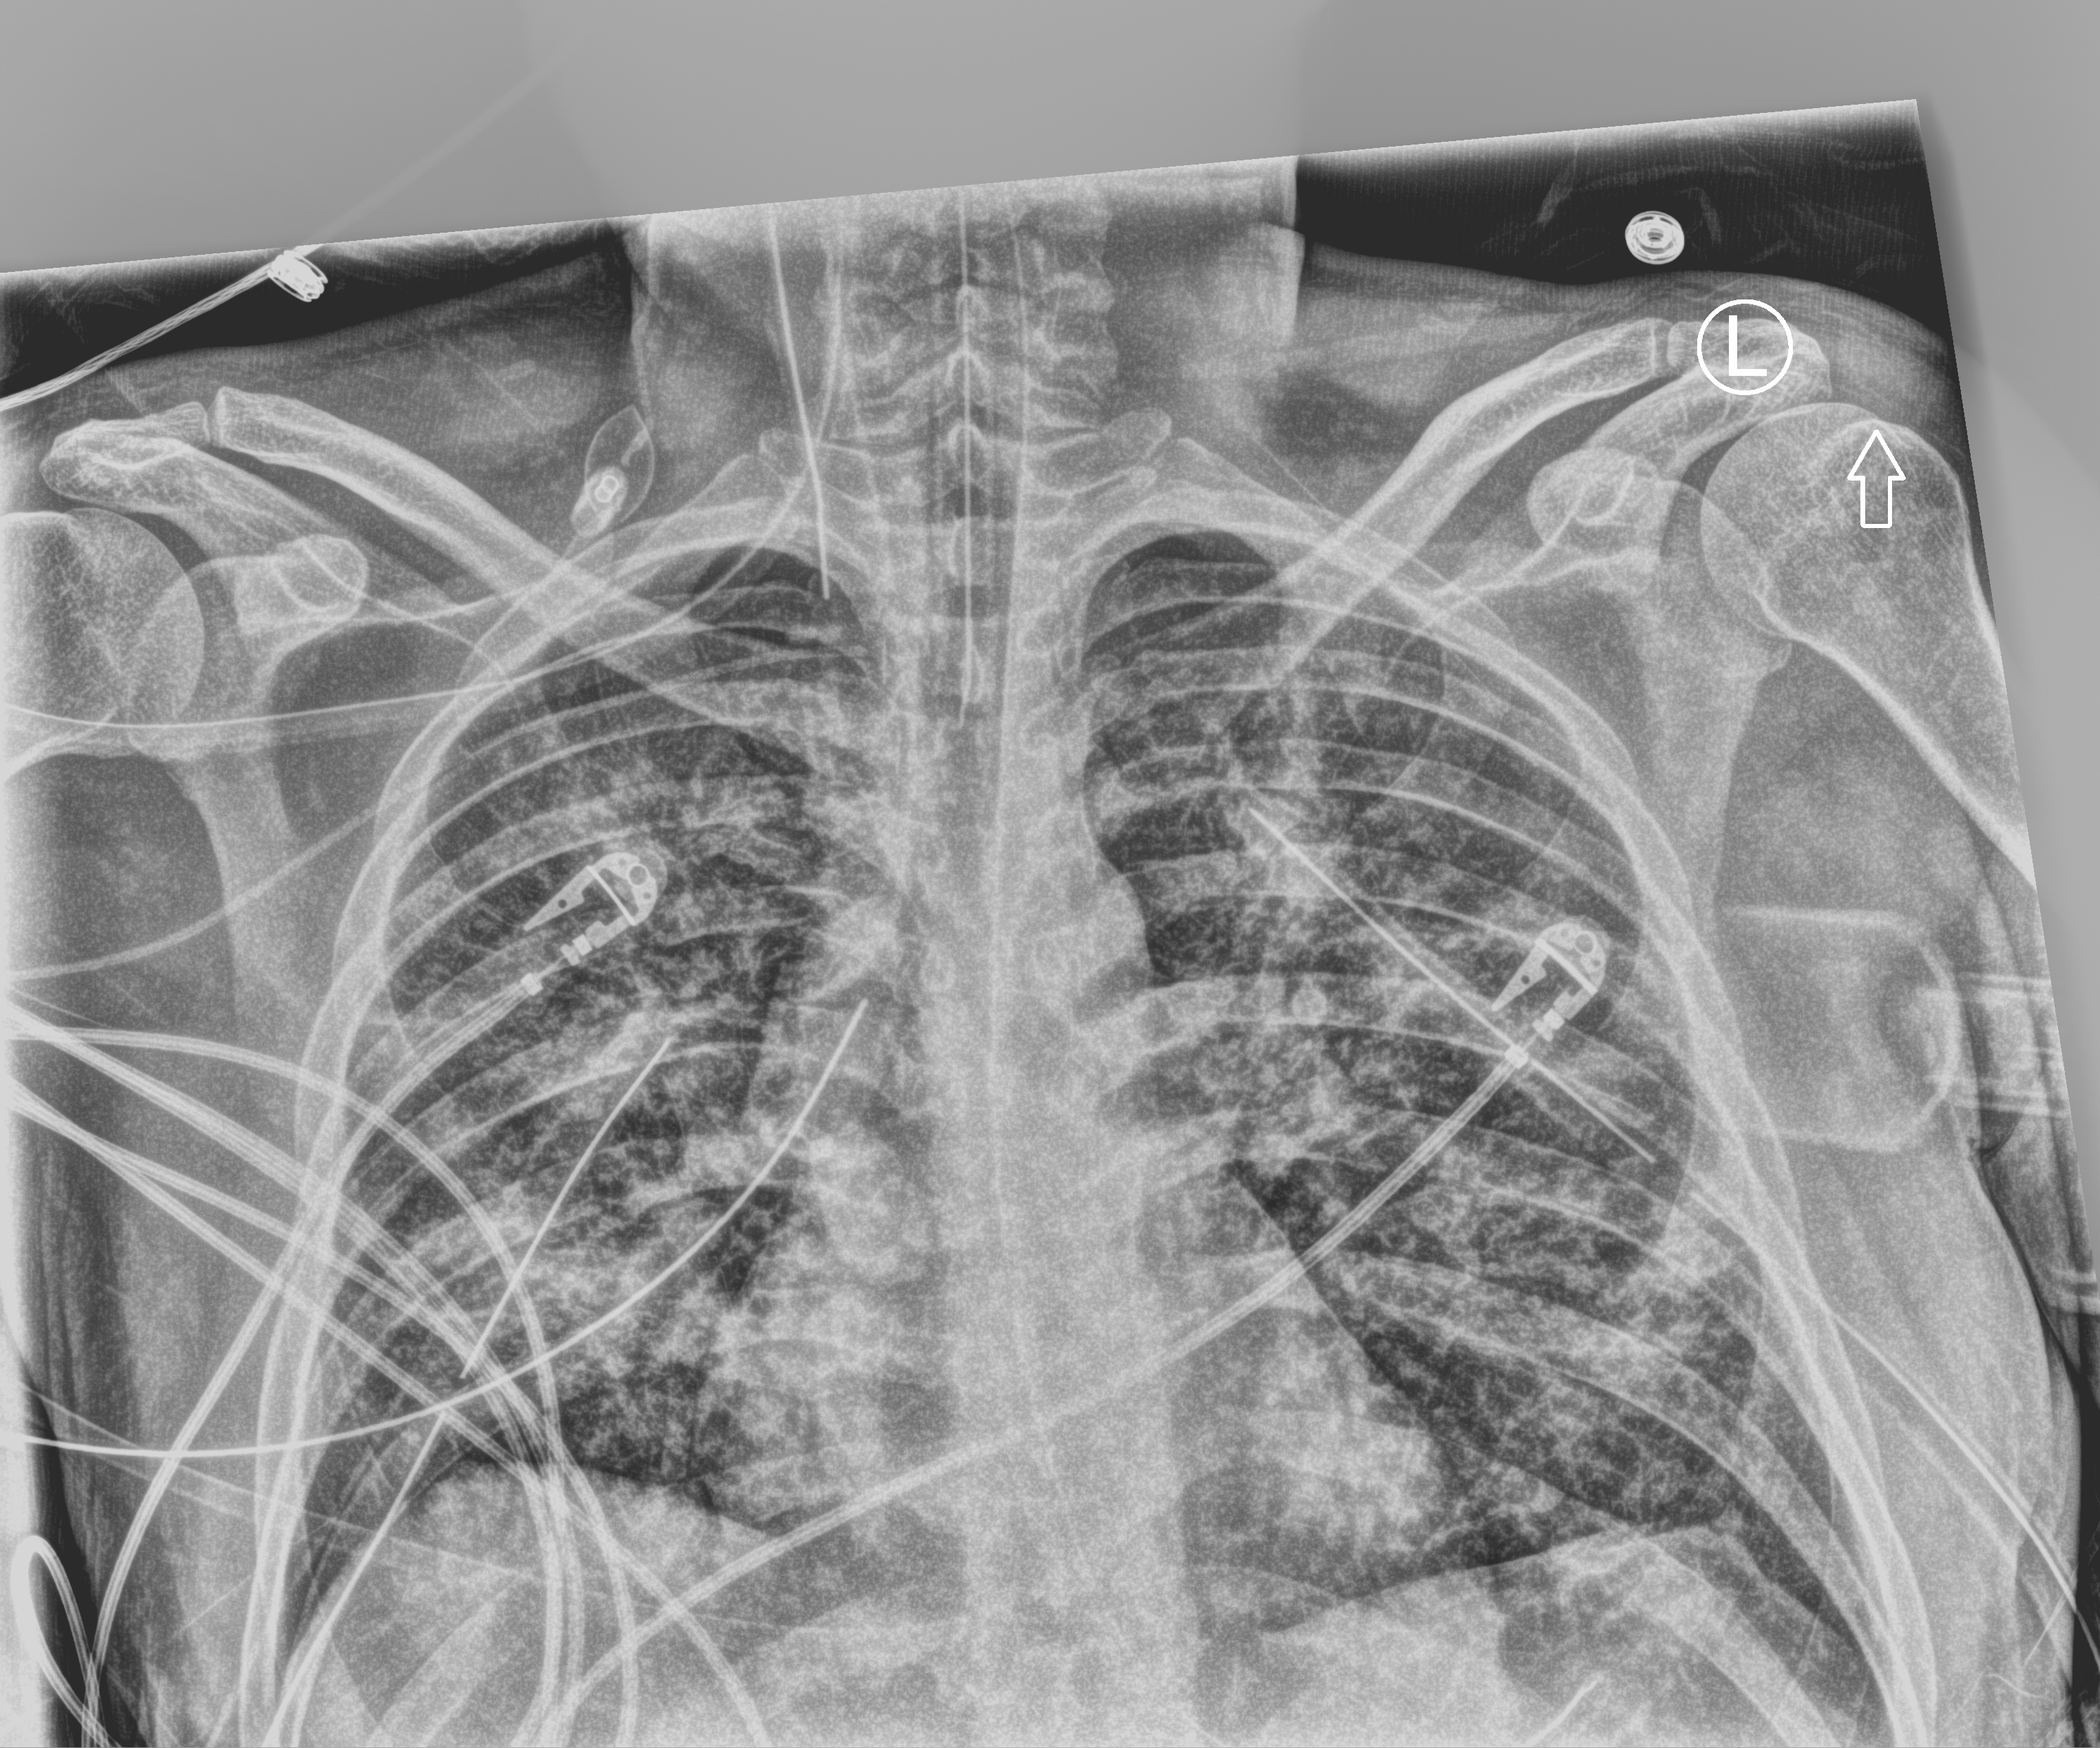
Bedside chest radiograph (computed radiography). Male patient hospitalised with COVID-19, age 18–59 years.
Hospital-stay facts (about this admission, not read from this image; timing relative to this image not recorded): mechanically ventilated during this hospital stay: yes; smoking status (admission record): never.